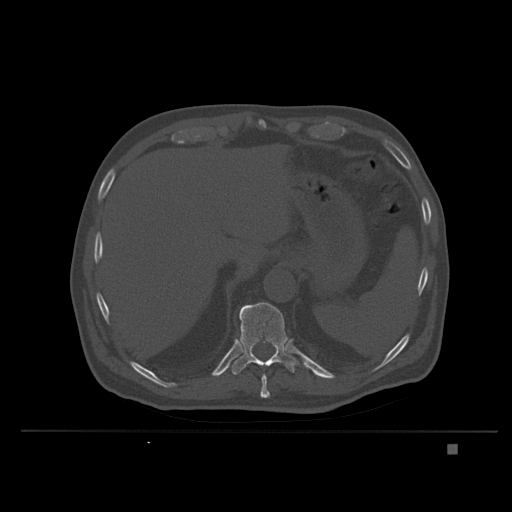
CT including the spine, one axial slice. Slice 181 of 435 in the series (ordered by position). Bone window (W 1800 / L 400 HU). 512 × 512 image matrix. Male patient, age 73 years. Case-level facts recorded for this patient, not image findings: primary cancer: skin.
Annotated regions visible in this slice (semi-automatic segmentation, software-assisted and operator-edited):
- T10 vertebra: bounding box (x1, y1, x2, y2) in pixels: (260, 374, 270, 398)
- T11 vertebra: (231, 302, 299, 375)